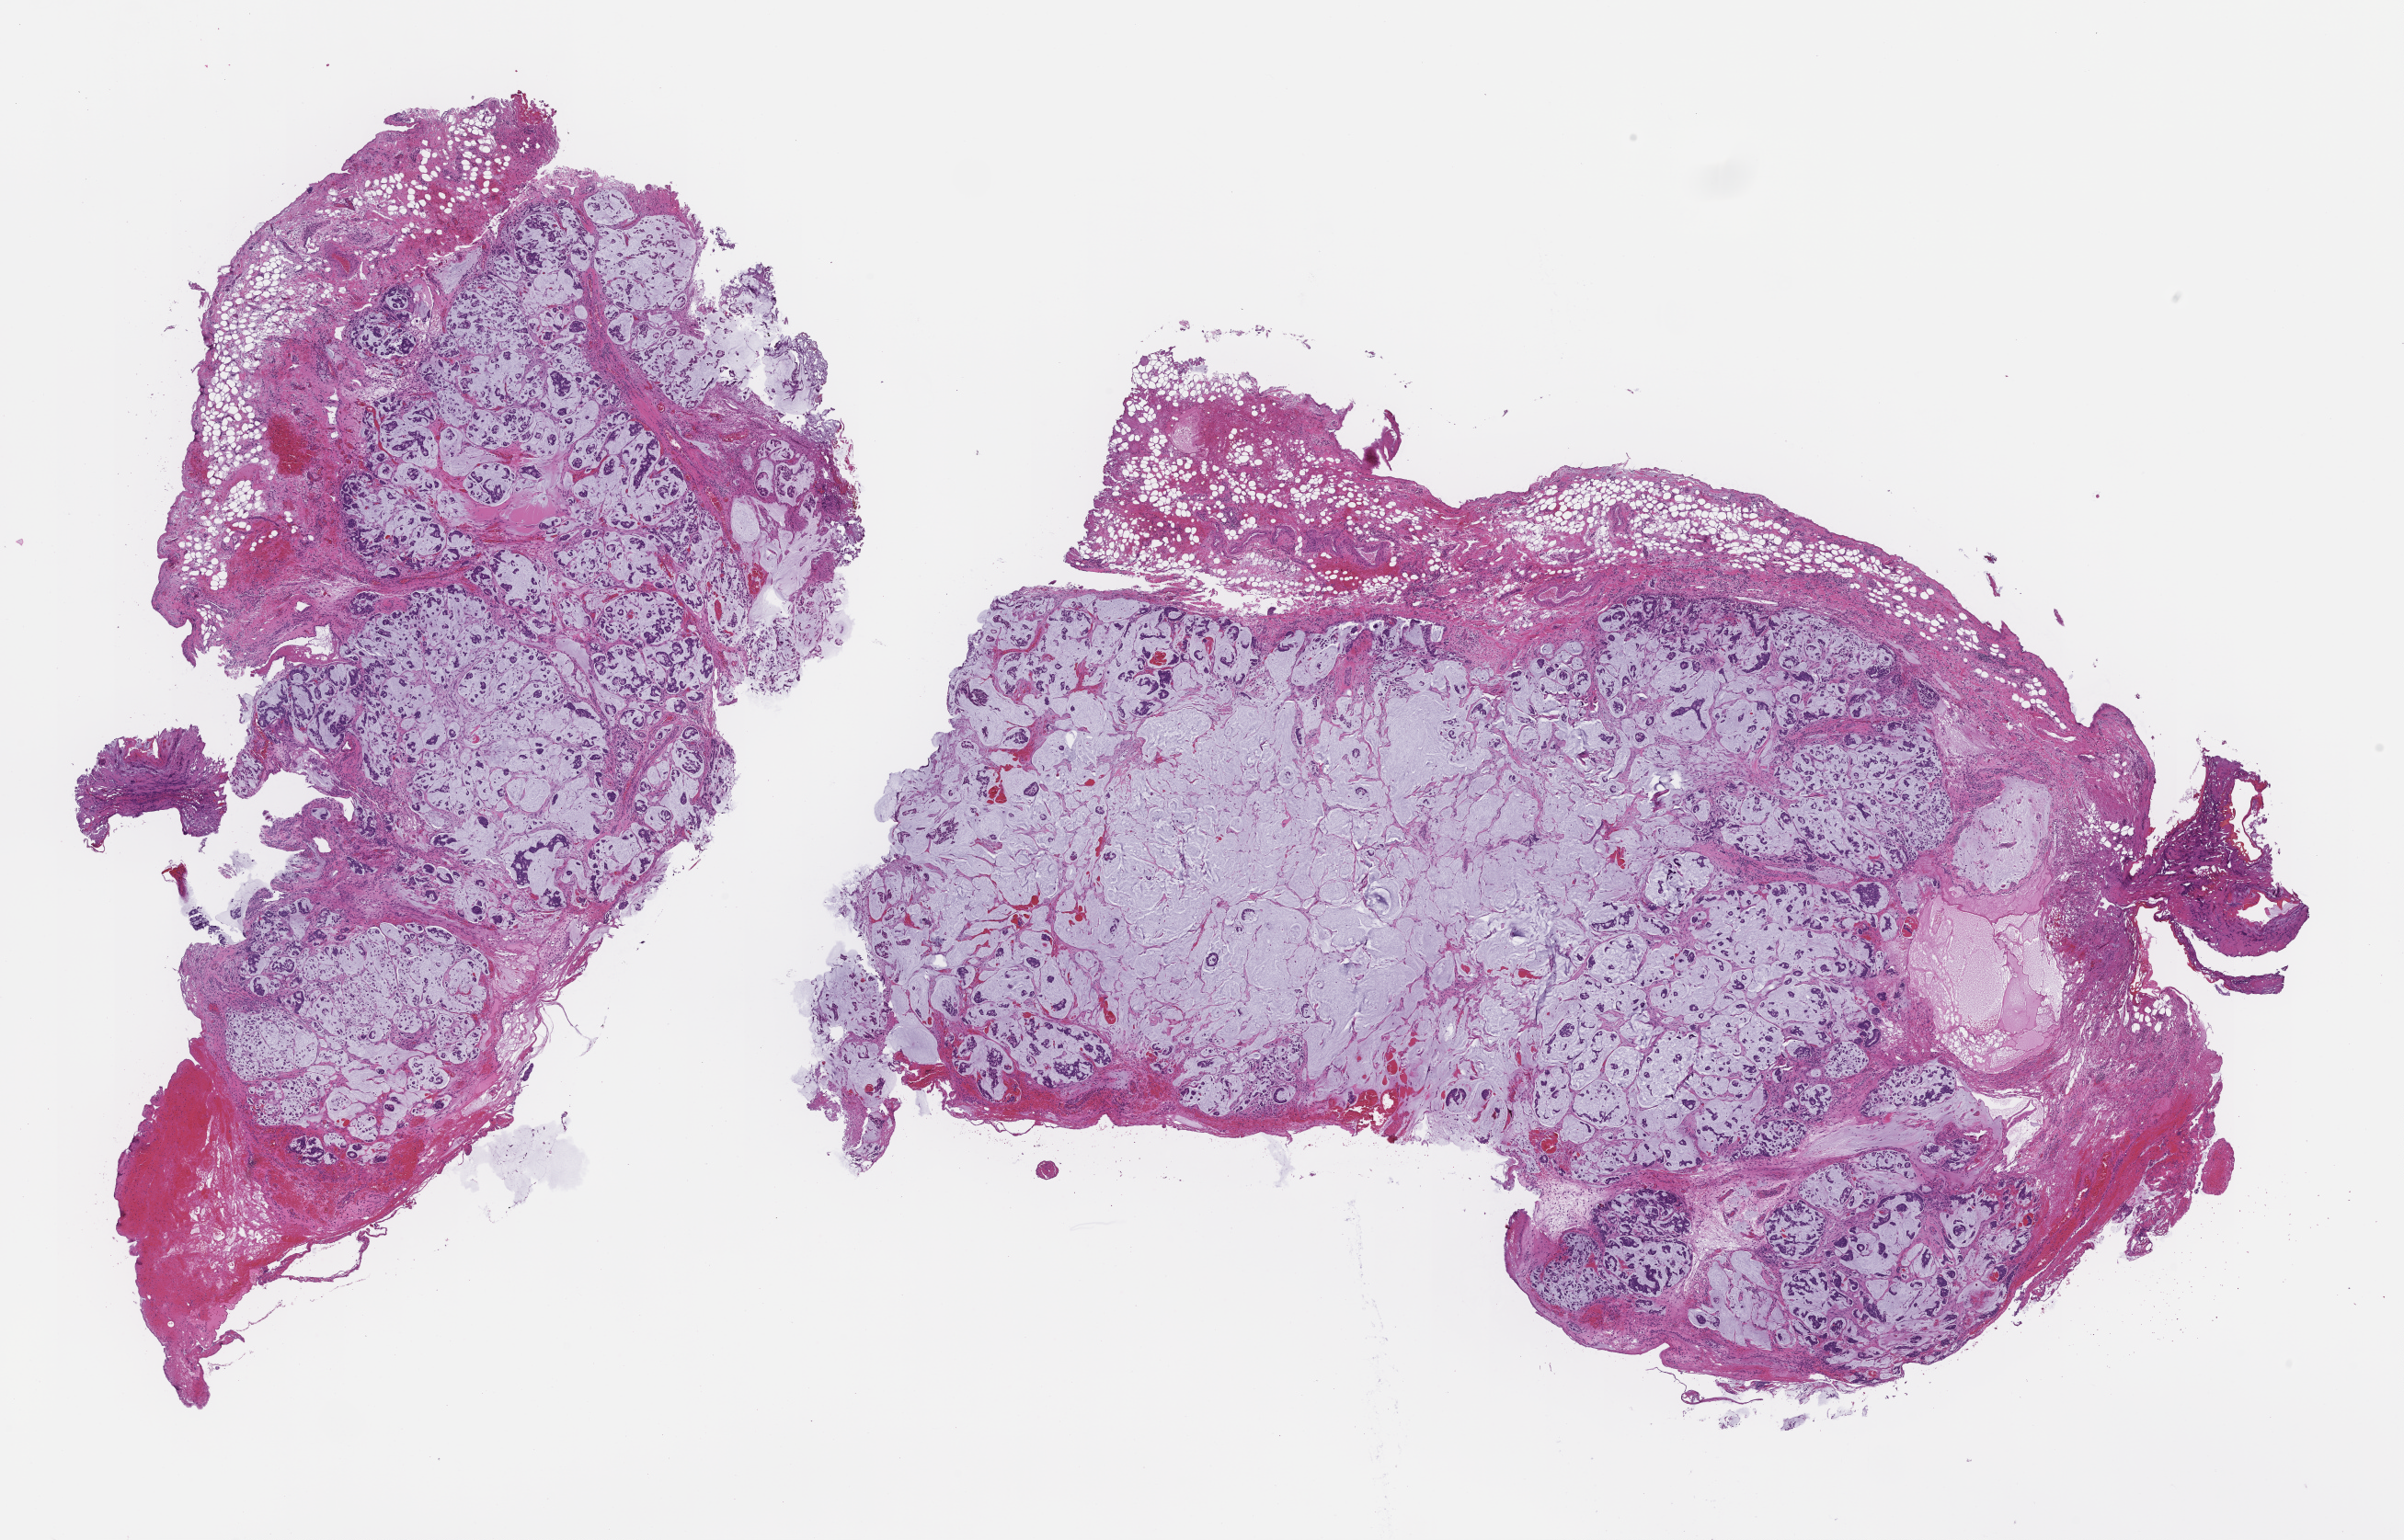
Digitized hematoxylin and eosin (H&E)-stained section — a low-resolution overview of the entire scanned area, about 21.1 x 13.5 mm, FFPE section, tissue site: colon, collected at disease progression. Patient: male.
• patient diagnosis: Colorectal Carcinoma